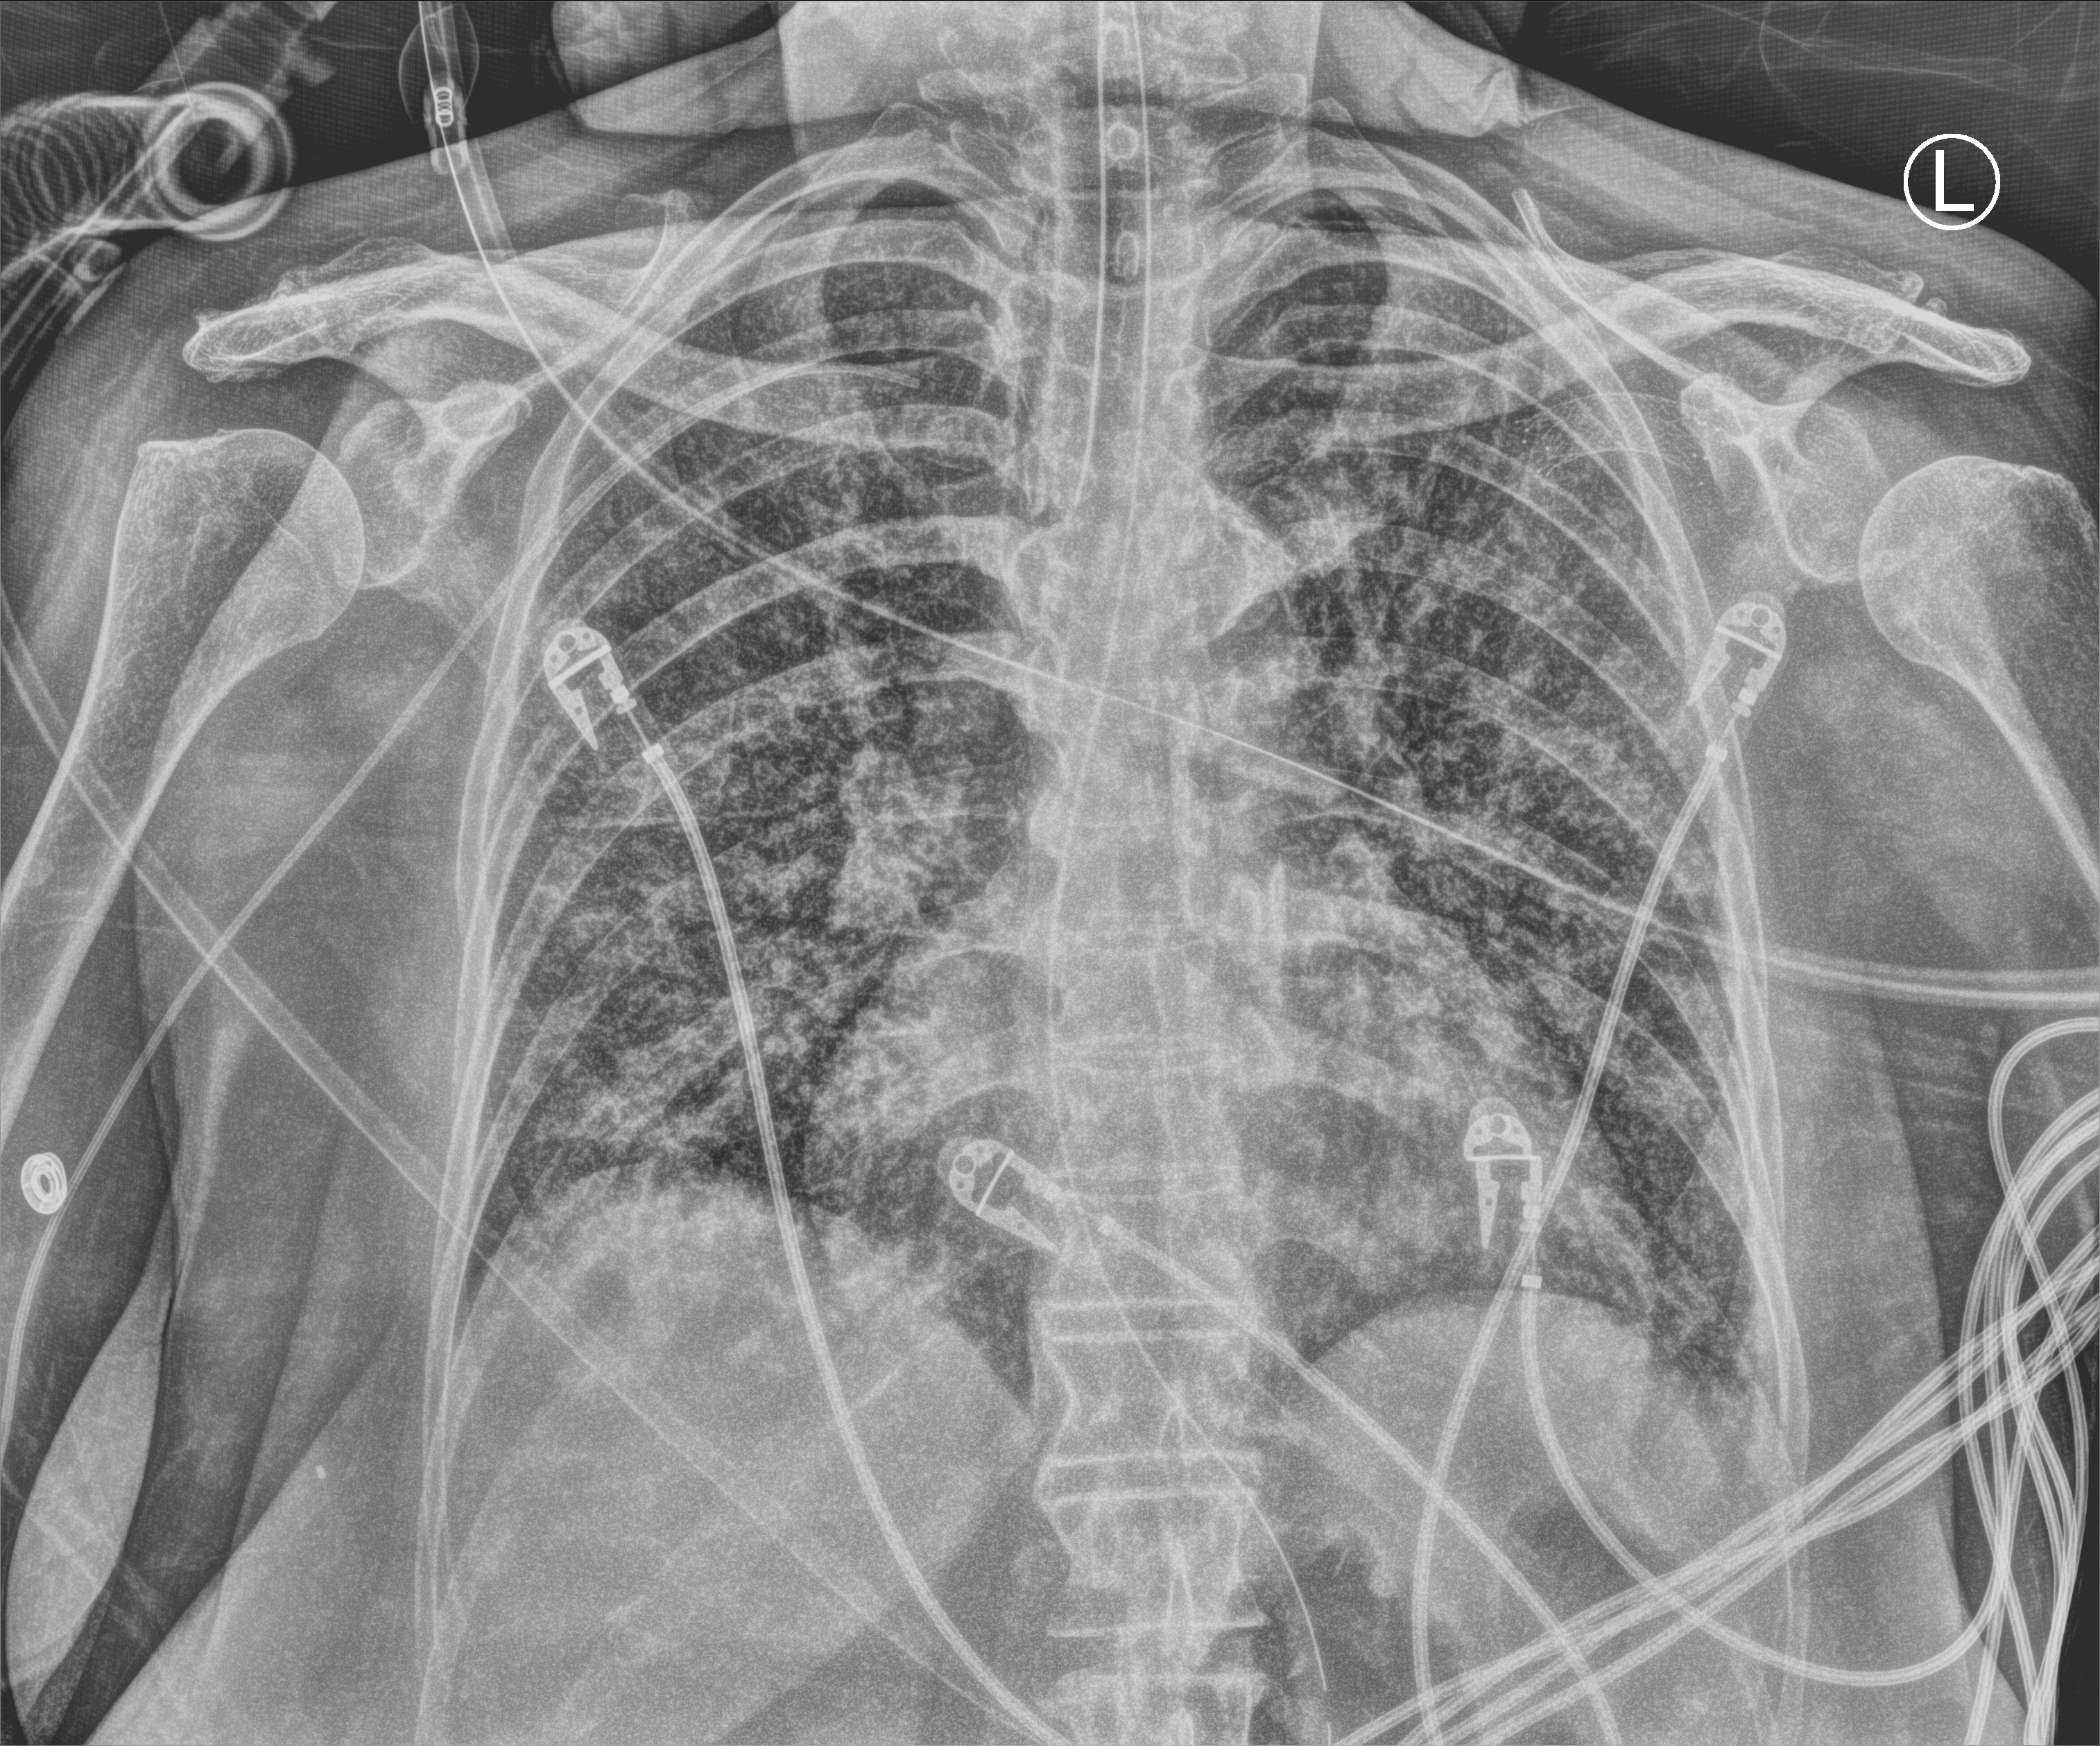
Portable chest radiograph; anteroposterior (AP) projection. Female patient hospitalised with COVID-19, age 60–74 years.
From the hospital-stay record, not from the radiograph (when in the stay this image was taken is not recorded): mechanically ventilated during this hospital stay: yes; length of hospital stay: 23 days; COPD (admission record): no.